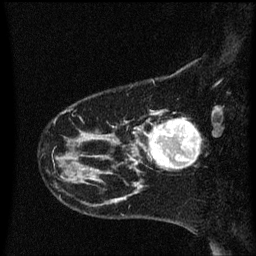
Breast MRI (dynamic contrast-enhanced), one sagittal slice. Slice 13 of 60 in the series (ordered by position). Dynamic contrast-enhanced series, image 2 of 3 at this slice position (ordered by acquisition). 1.5 T. TE 4.2 ms, TR 8.4 ms. 2 mm slice thickness. 256 × 256 image matrix, field of view 200 × 200 mm. Female patient, age 41 years. From the clinical record (not read from this slice): setting: breast cancer imaged before/during neoadjuvant chemotherapy; receptor status: triple-negative.
Structures marked on this image (semi-automatically segmented with operator editing):
- analysis volume of interest (the breast-tissue region the enhancement analysis was run in; not a lesion): bounding box <138,120,200,173> (left, top, right, bottom; pixels)
- tumour enhancement mask (voxels above the 70 % enhancement threshold inside the analysis volume of interest): <146,120,199,169>